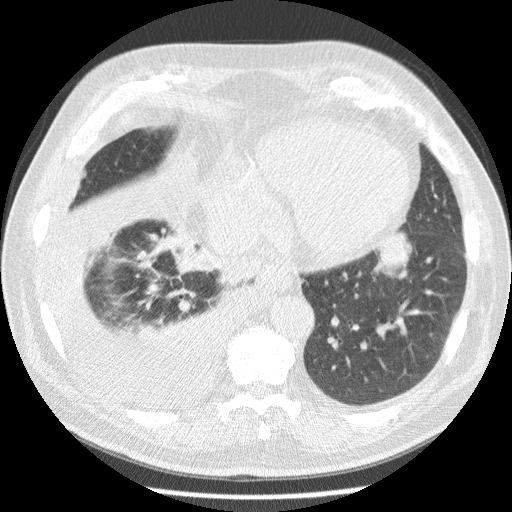
Chest CT (low-dose screening protocol), one axial image. Third annual screen. Lung window (W 1500 / L -600 HU). 2.5 mm slice thickness. Slice 62 of 180 in the series. 512 × 512 image matrix. Male participant, aged 63 years at enrolment. Current smoker at enrolment.
- Lesion marked by an expert reader, box from (x=349, y=225) to (x=417, y=297) px.
- Reader record for this screening exam (exam-level; its link to the box is not recorded): non-calcified nodule or mass ≥4 mm, left lower lobe, 34 × 31 mm, smooth margins, soft tissue attenuation, pre-existing on the prior screen: yes; interval growth: yes.
- Official screen result: positive, other.
- Participant outcome: lung cancer diagnosed 30 days after this screen — squamous cell carcinoma, NOS, left lower lobe, stage IB (AJCC 6th edition), 48 mm at pathology.